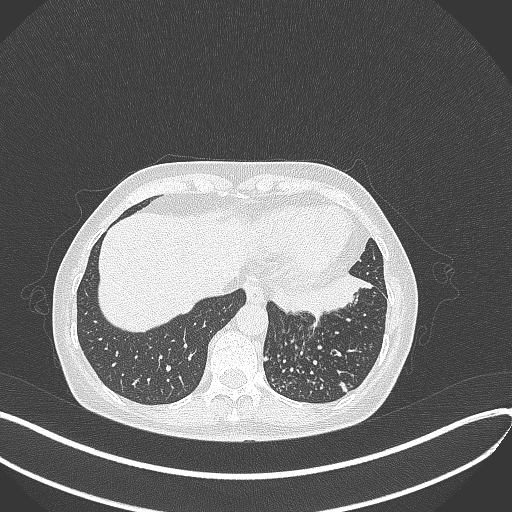
Chest CT, one axial slice; position 95 of 429 along the scan axis; reconstruction kernel B70f; 100 kVp; lung window (W 1500 / L -600 HU); 512 × 512 image matrix. Female patient, age 63 years. From the clinical record (not read from this slice): clinical TNM (as recorded): T1b N0 M0; histopathological grade: G2-3.
Annotated regions visible in this slice (rectangle marked by the reading radiologist):
- lung tumour (recorded histology: adenocarcinoma): bounding box [x1, y1, x2, y2] px = [272, 272, 372, 314]